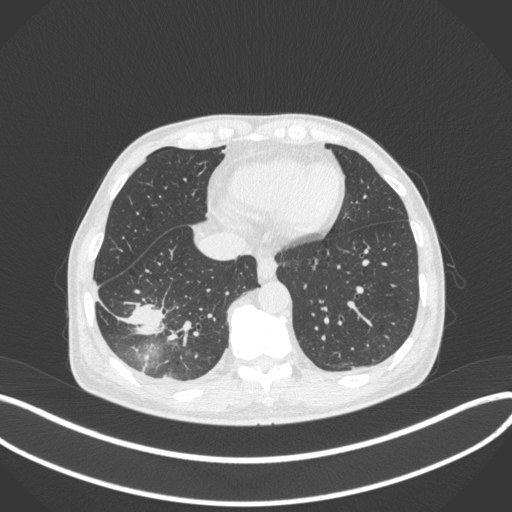
Chest CT, one axial slice. Slice 102 of 385 in the series (ordered by position). Reconstruction kernel B31f. 120 kVp. Lung window (W 1500 / L -600 HU). 1 mm slice thickness. 512 × 512 image matrix, field of view 400 × 400 mm. Male patient, age 64 years. Case-level facts recorded for this patient, not image findings: clinical TNM (as recorded): T3 N0 M0; histopathological grade: G2-3.
Outlined on this slice (bounding box drawn by a radiologist):
- lung tumour (recorded histology: adenocarcinoma): bounding box <120,294,170,342> (left, top, right, bottom; pixels)